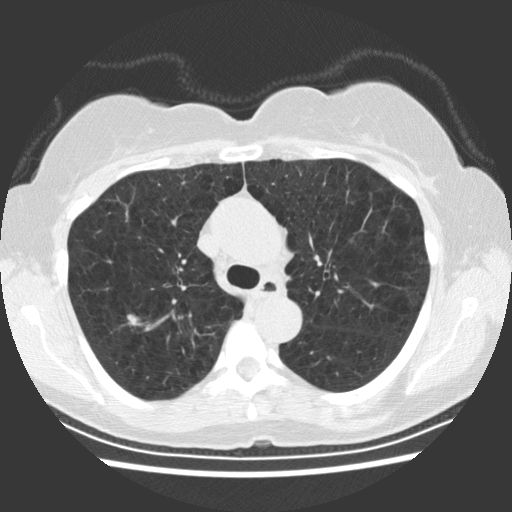
Low-dose screening chest CT, one axial slice. Slice 166 of 234 in the series (ordered by position). 120 kVp. Lung window (W 1500 / L -600 HU). 2.5 mm slice thickness. 512 × 512 image matrix, field of view 330 × 330 mm.
Annotated regions visible in this slice (outlined manually by an expert reader):
- lesion 1 (tumor, upper lobe of right lung): box from (x=127, y=314) to (x=139, y=326) px